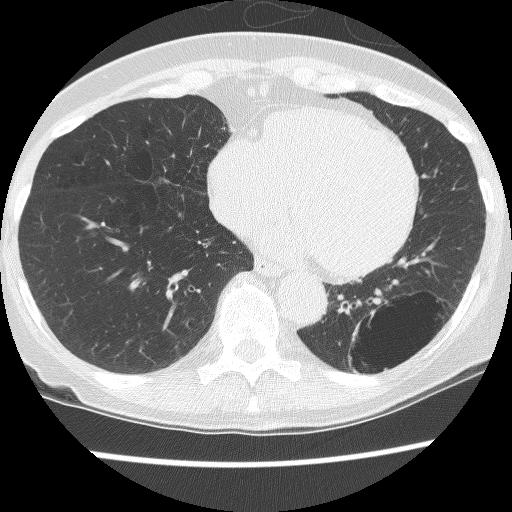
Low-dose screening chest CT, axial slice, third annual screen, lung window (W 1500 / L -600 HU), 2.5 mm slice thickness, lung (sharp) reconstruction kernel (BONE), 120 kVp. Female, age 61 years at enrolment.
• Expert-annotated lung lesion, bounding box [x1, y1, x2, y2] px = [331, 291, 446, 389].
• The screening reader recorded 2 non-calcified nodules or masses ≥4 mm on this exam (left lower lobe, left lower lobe); which of them this box marks is not recorded.
• Official screen result: positive, no significant change: stable abnormalities potentially related to lung cancer, unchanged since the prior screening exam.